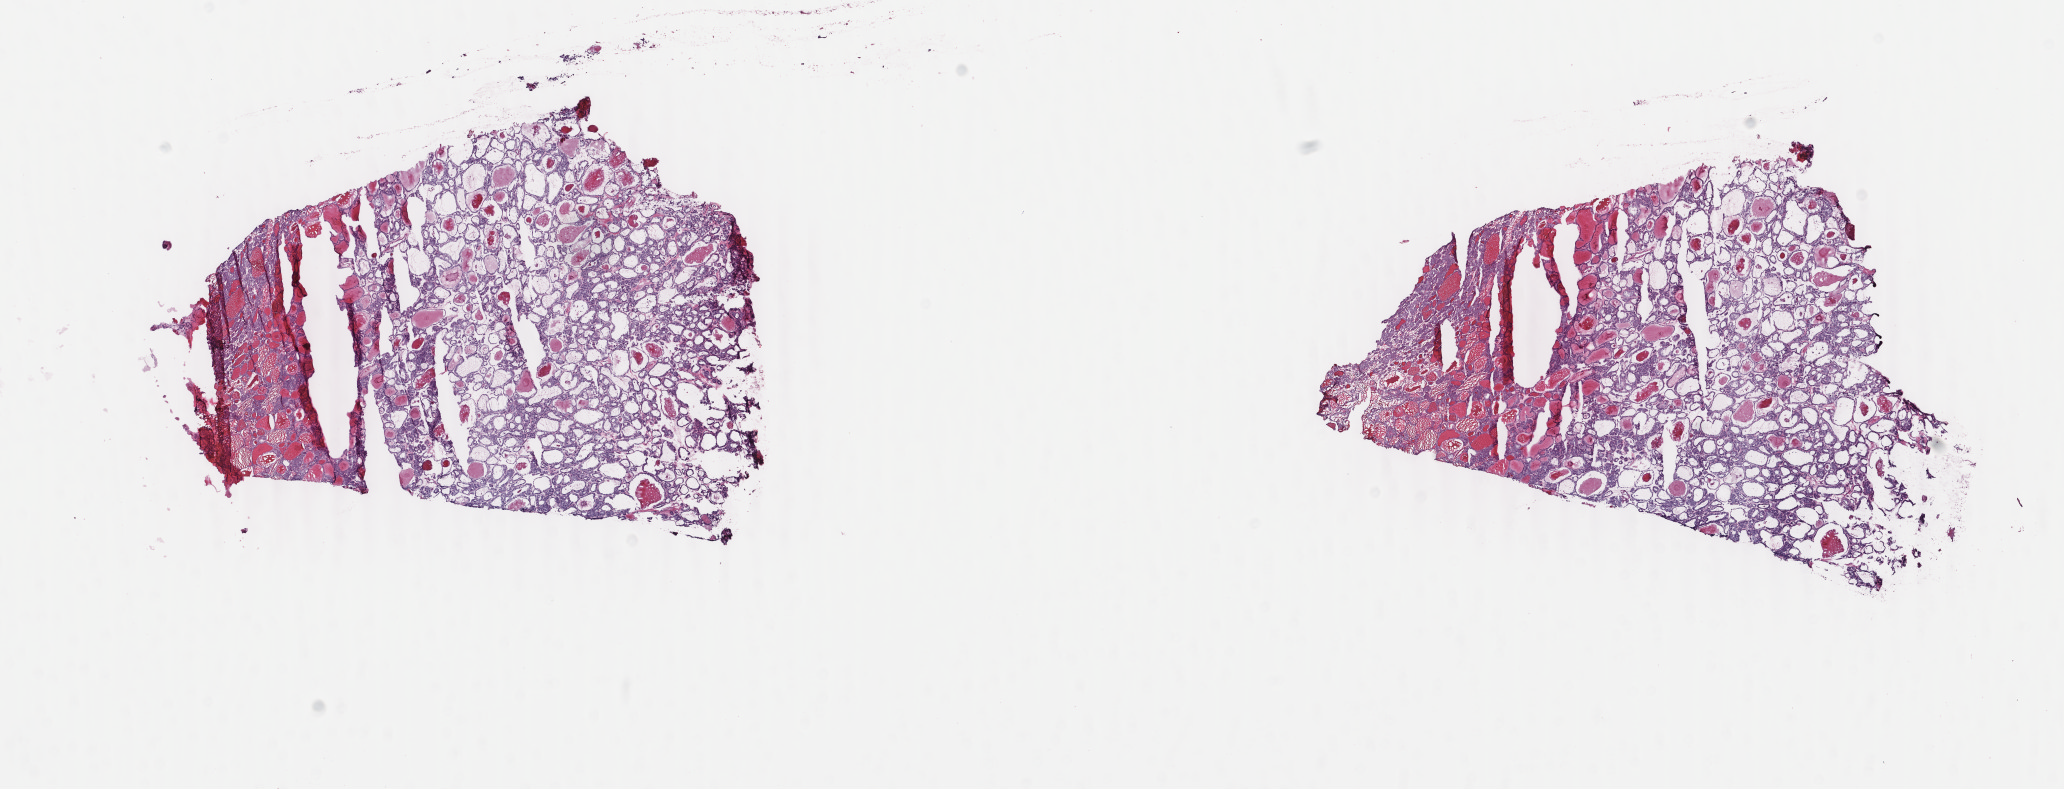
Whole-slide histology image, Hematoxylin and eosin (H&E) stained, shown as a low-resolution overview of the whole scanned area (about 16.4 x 6.3 mm, acquisition: 40x scan). Frozen section. Primary tumour sample from the thyroid. Patient: female, age at initial diagnosis 28 years. Composition of this section per pathologist review: tumour cells 100%, tumour nuclei 95%, normal cells 0%, stromal cells 0%, necrosis 0%. Inflammatory infiltration, as recorded: lymphocyte infiltration 0%, monocyte infiltration 0%, neutrophil infiltration 0%.
* histologic diagnosis: Papillary carcinoma, follicular variant (thyroid gland)
* TNM: T1b N0 M0
* AJCC pathologic stage: I
* lymph nodes positive (case pathology): 0 of 5 examined